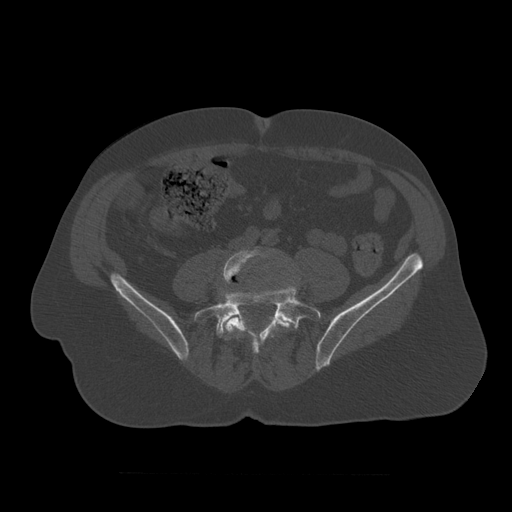
CT including the spine, one axial slice; slice 263 of 450 in the series (ordered by position); reconstruction kernel STANDARD; 120 kVp; bone window (W 1800 / L 400 HU); 1.25 mm slice thickness; 512 × 512 image matrix, field of view 405 × 405 mm. Patient age 75 years. Case-level facts recorded for this patient, not image findings: primary cancer: prostate.
Outlined on this slice (semi-automatically segmented with operator editing):
- L4 vertebra: bounding box [x1, y1, x2, y2] px = [221, 248, 292, 357]
- L5 vertebra: [194, 287, 323, 340]